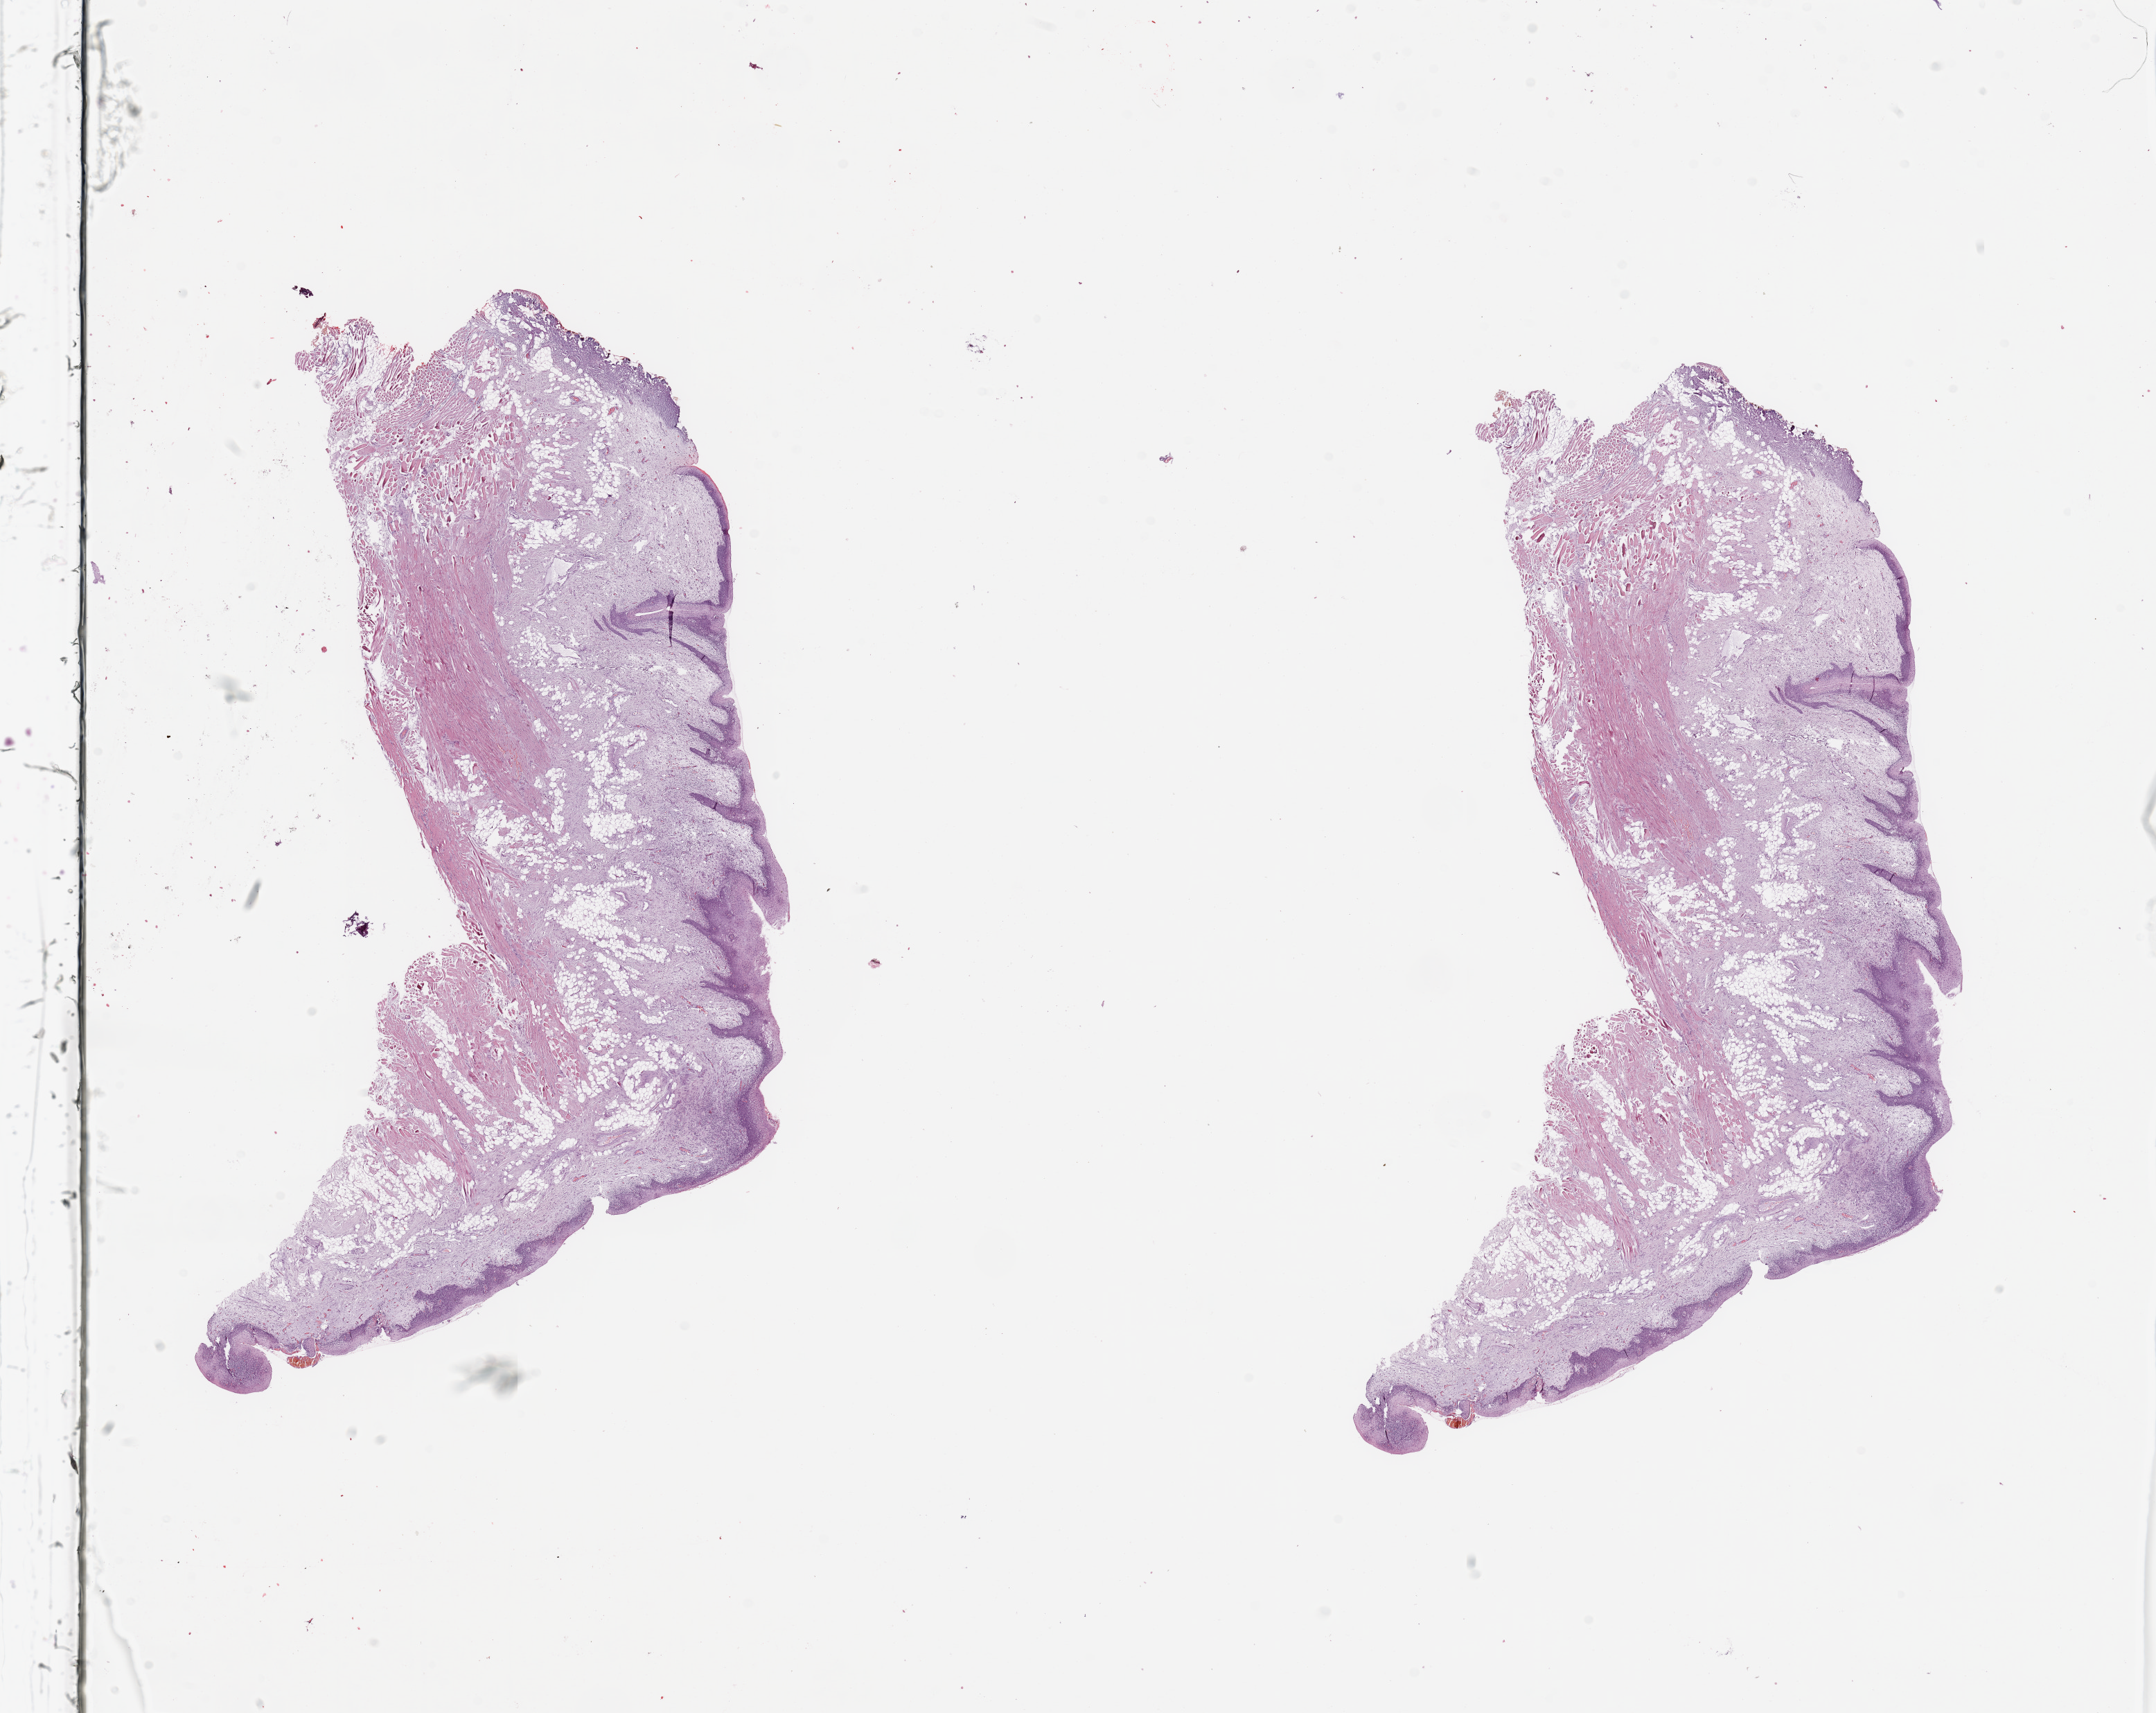
H&E-stained whole-slide image — low-resolution overview of the scanned area, about 24.6 x 19.5 mm. Normal (non-tumour) tissue sample, sampled site: floor of mouth. 70-year-old female patient.
This section: normal (non-tumour) tissue from the same patient. Patient diagnosis: Squamous cell carcinoma, NOS (floor of mouth, NOS).